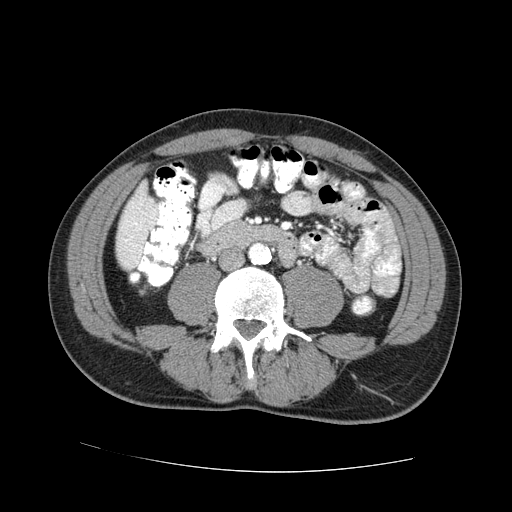
Contrast-enhanced abdominal CT (liver protocol), one axial slice. Position 6 of 73 along the scan axis. Reconstruction kernel STANDARD. 100 kVp. One of 2 acquisitions stored at this slice position. Soft-tissue window (W 400 / L 40 HU). 2.5 mm slice thickness. 512 × 512 image matrix, field of view 380 × 380 mm. Case-level facts recorded for this patient, not image findings: diagnosis: hepatocellular carcinoma (patient treated with transarterial chemoembolisation; whether this scan precedes or follows treatment is not stated here); TNM stage (as recorded): Stage-IVA; Child-Pugh class: A.
Structures marked on this image (semi-automatically segmented with operator editing):
- liver parenchyma outside the tumour (the mass and vessels are separate outlines, so this box may not span the whole liver): bounding box <116,182,156,268> (left, top, right, bottom; pixels)
- liver vessels: <126,222,137,241>